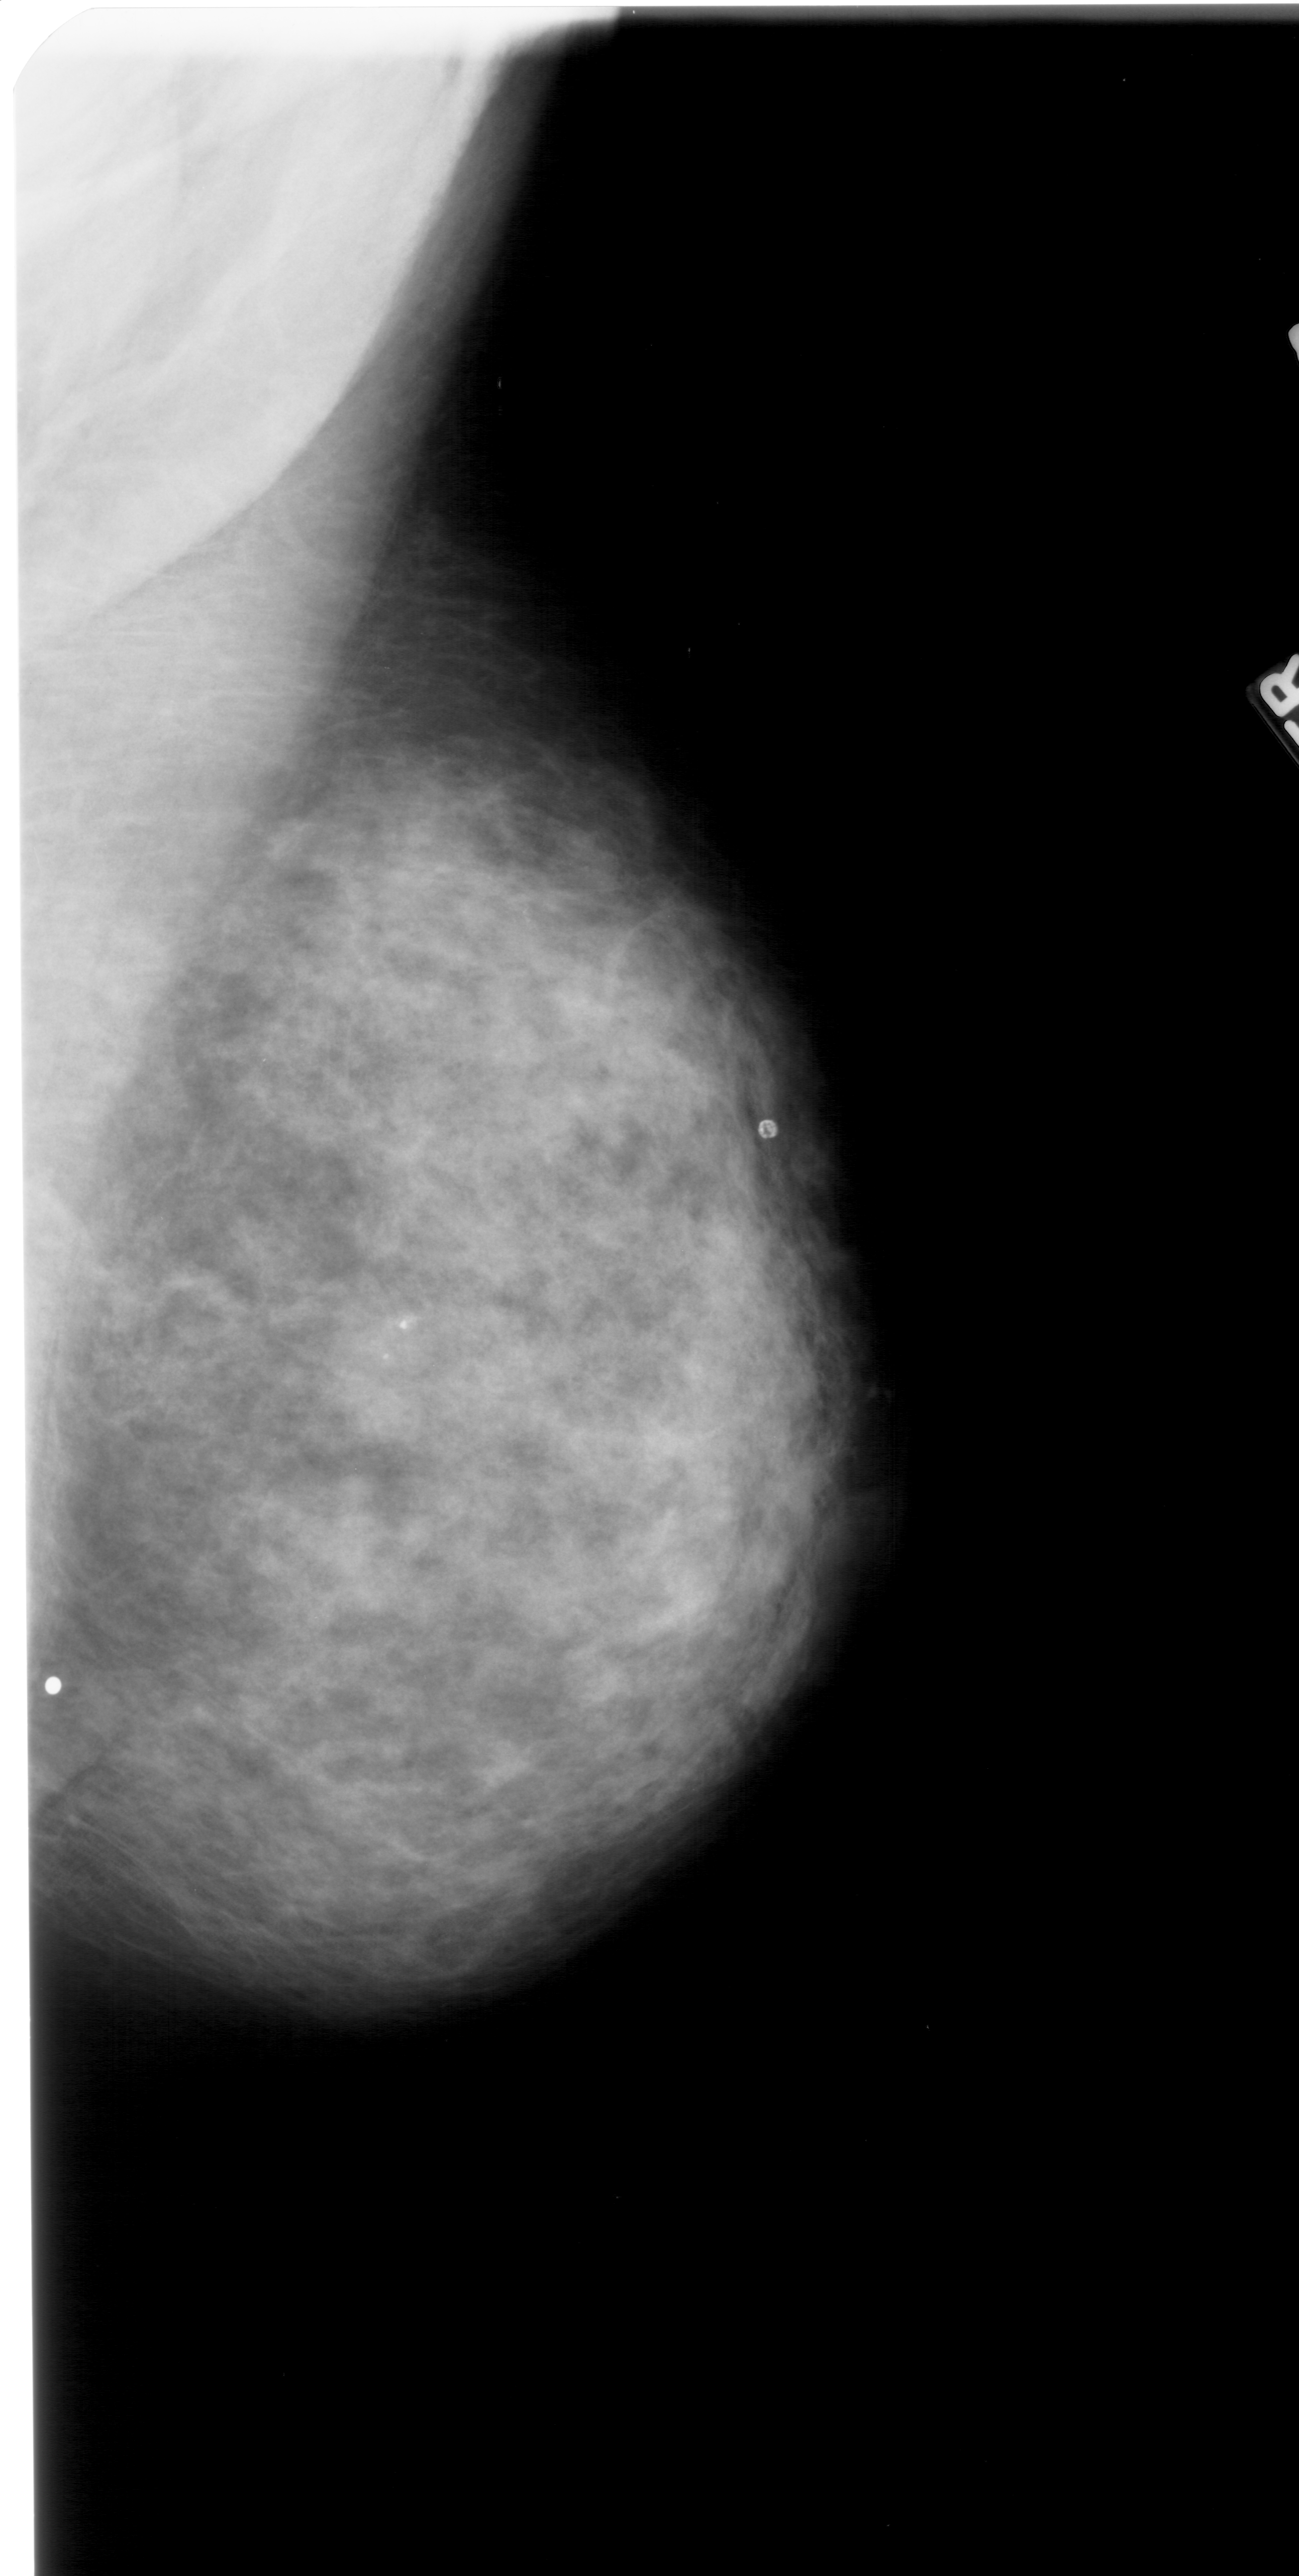
Digitized screen-film mammogram; right breast; MLO view; BI-RADS breast density category 3 (scale 1–4).
Calcifications, morphology pleomorphic, distribution clustered; BI-RADS assessment category 4; pathology (as recorded): malignant.